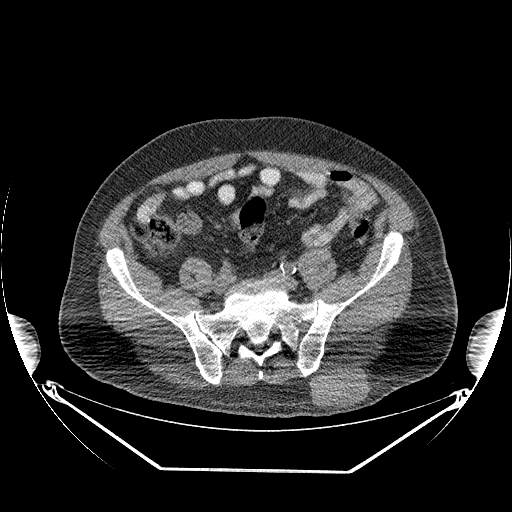
CT of an extremity soft-tissue mass (from a PET/CT study), one axial slice. Slice 89 of 267 in the series (ordered by position). Reconstruction kernel STANDARD. Soft-tissue window (W 400 / L 40 HU). 512 × 512 image matrix. Male patient. Case-level facts recorded for this patient, not image findings: histological type: pleiomorphic leiomyosarcoma; grade: high; site of the primary tumour: left buttock.
Outlined on this slice (expert contour drawn on MRI and transferred to this co-registered scan by the dataset authors):
- gross tumour volume including surrounding oedema: bounding box [x1, y1, x2, y2] px = [311, 368, 369, 408]
- gross tumour volume (mass): [311, 368, 368, 408]